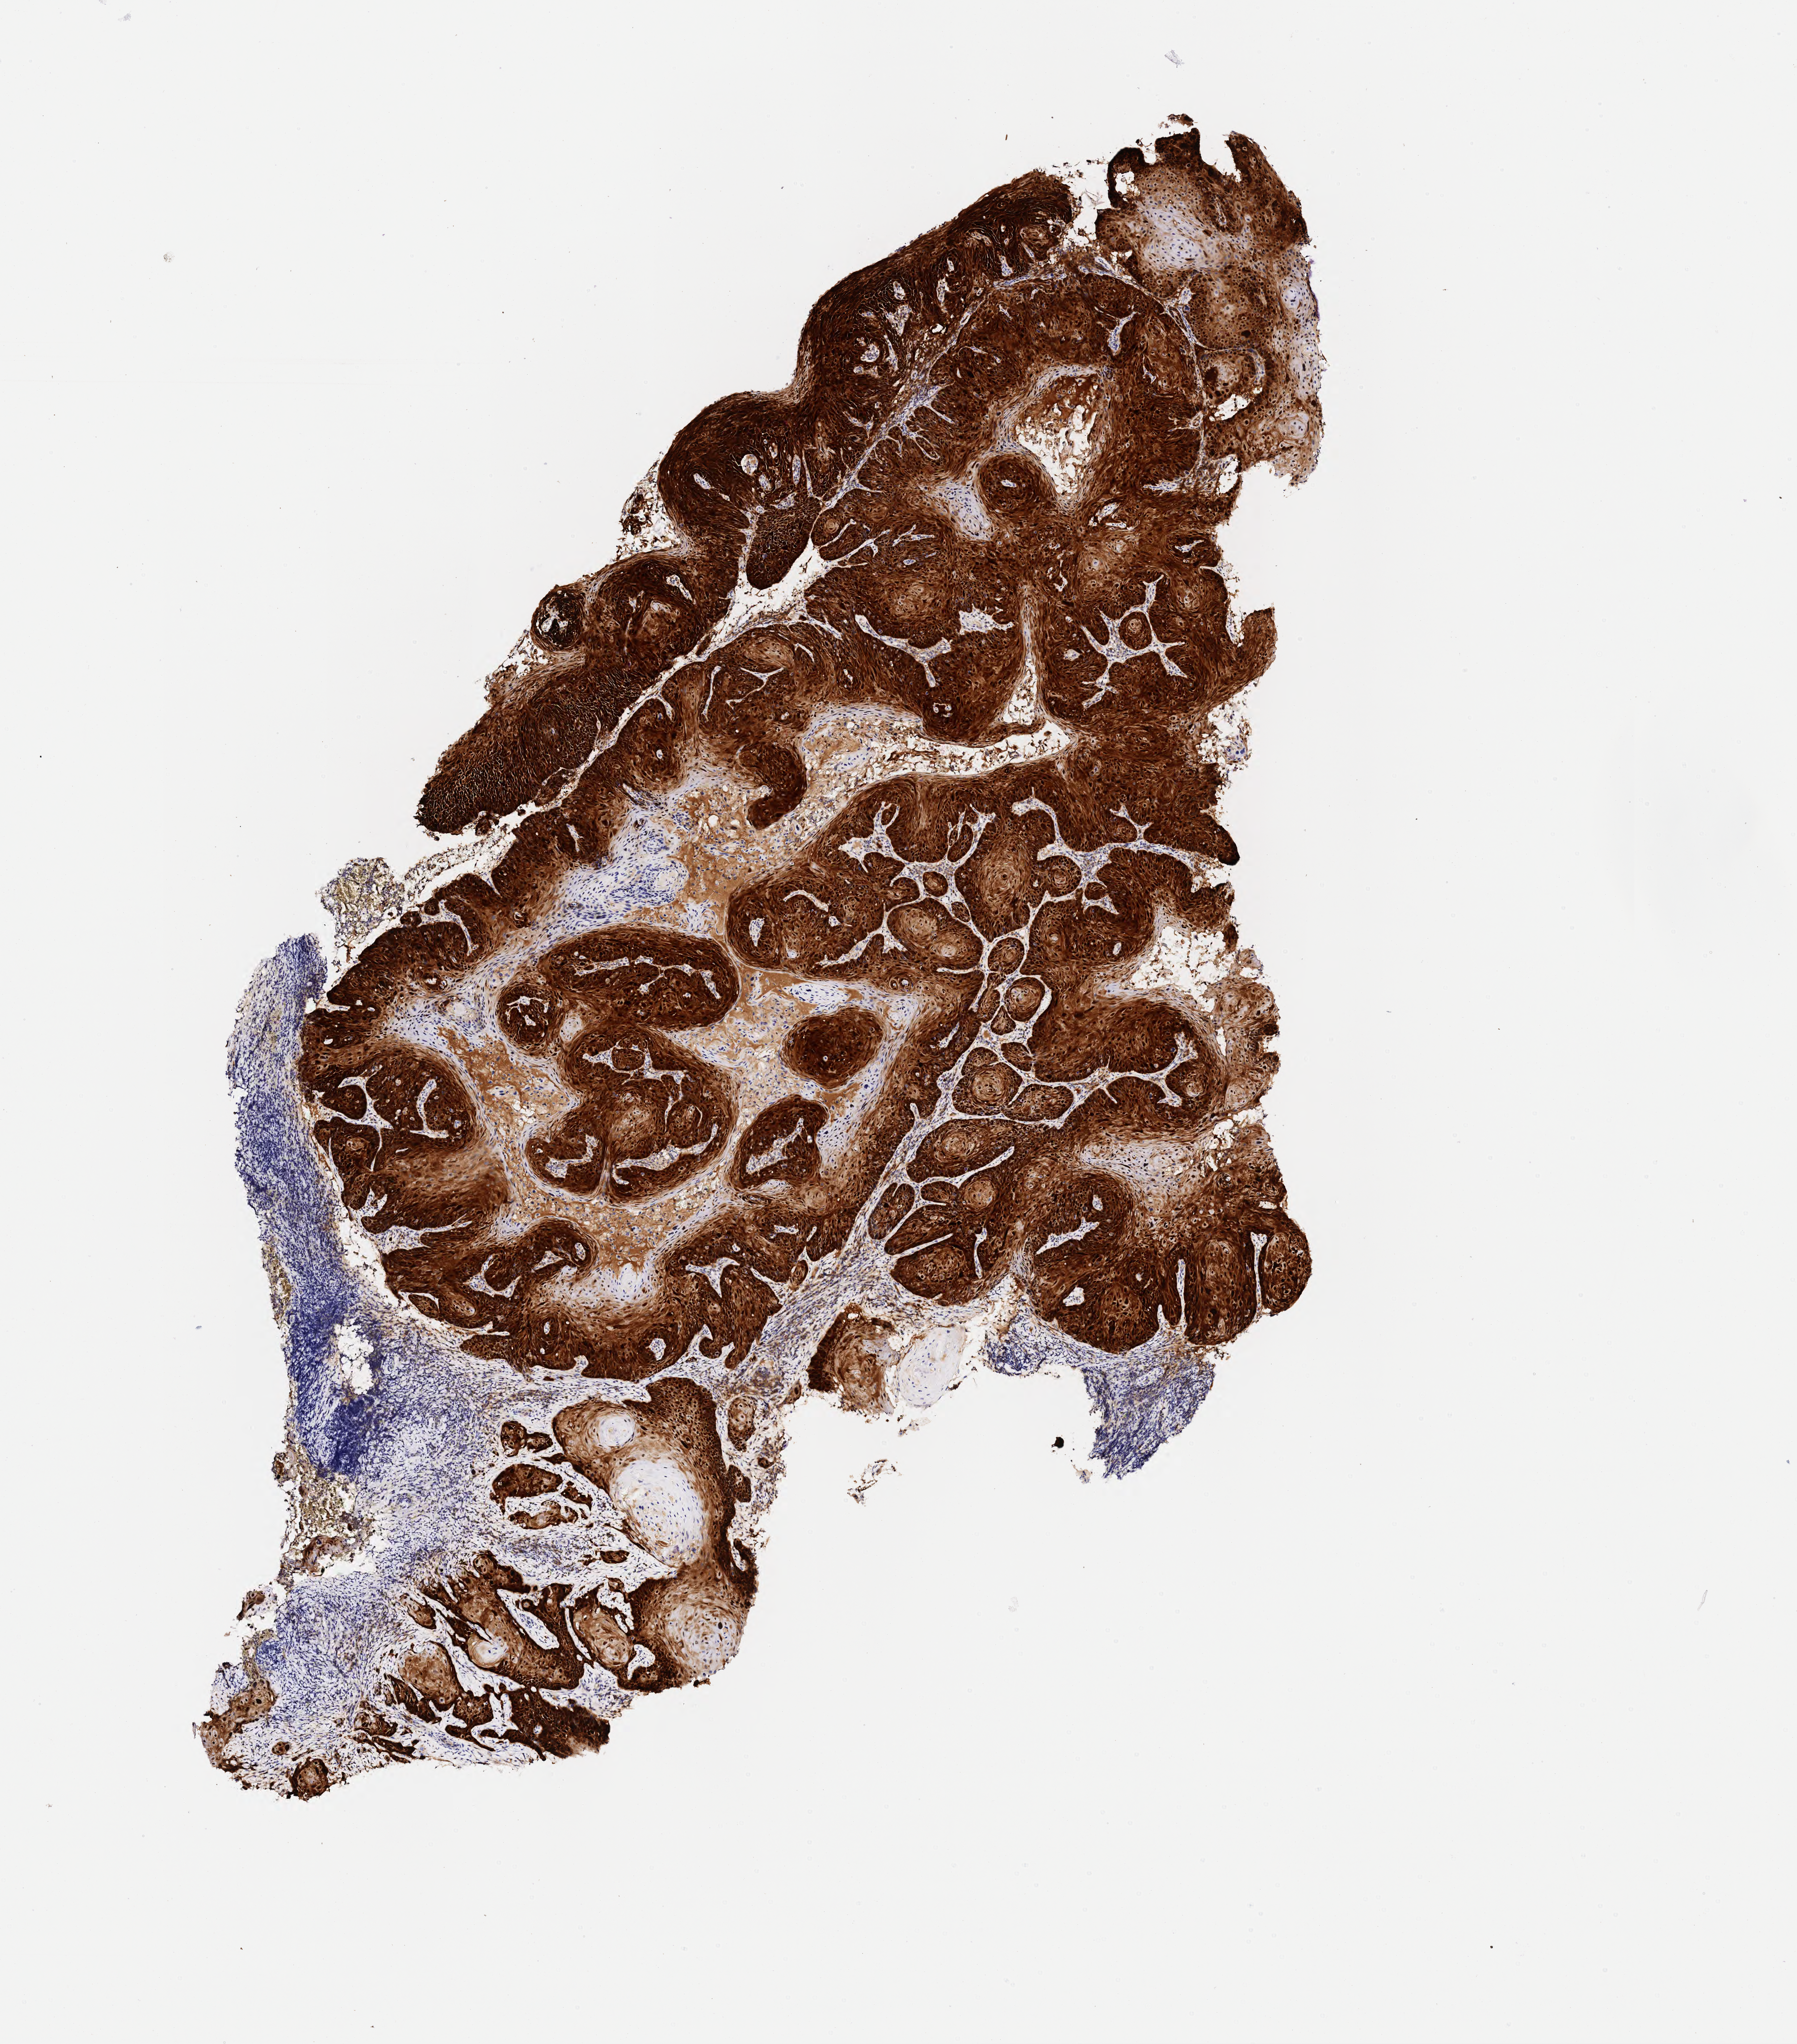
Immunohistochemistry (IHC) whole-slide image stained for p16 (p16INK4a) — a low-resolution overview of the entire scanned area, about 5.5 x 6.3 mm. Specimen: tumor tissue. Anatomic site: cervix. Patient female; aged 65.
Histologic diagnosis: Squamous cell carcinoma, keratinizing, NOS.